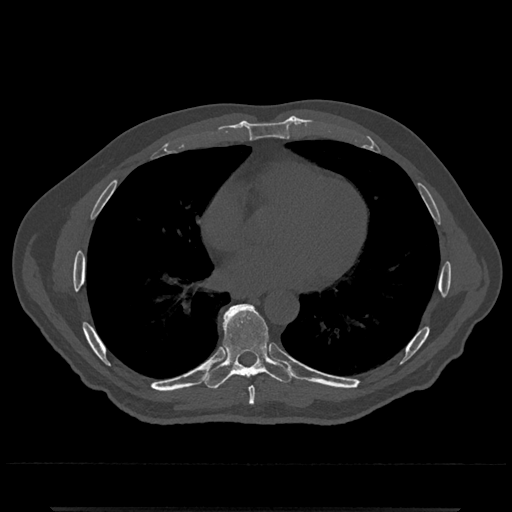
CT including the spine, one axial slice; position 680 of 797 along the scan axis; reconstruction kernel Br40s/3; 120 kVp; bone window (W 1800 / L 400 HU); 0.5 mm slice thickness; 512 × 512 image matrix, field of view 393 × 393 mm. Male patient, age 67 years. From the clinical record (not read from this slice): primary cancer: prostate.
Annotated regions visible in this slice (semi-automatic segmentation, software-assisted and operator-edited):
- T7 vertebra: box from (x=249, y=387) to (x=256, y=405) px
- T8 vertebra: (x=201, y=304)–(x=295, y=389)